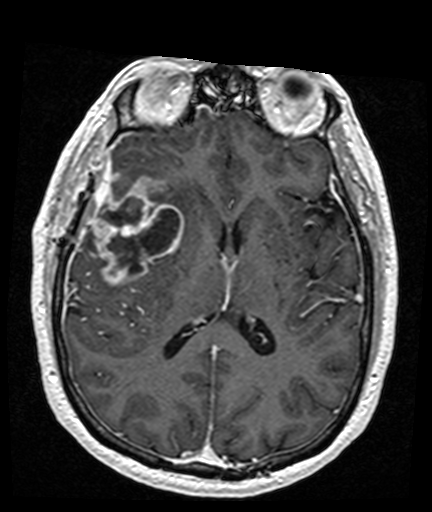
Brain MRI from a brain-tumour surgery series, one axial slice; T1-weighted post-contrast; 1 mm slice thickness; 432 × 512 image matrix. From the clinical record (not read from this slice): histopathology: Glioblastoma; WHO grade: 4; IDH mutation: no; tumour location: Right Frontal Temporal, Posterior Sylvian Fissure.
Annotated regions visible in this slice (outlined manually by an expert reader):
- tumour: bounding box [x1, y1, x2, y2] px = [93, 176, 183, 288]